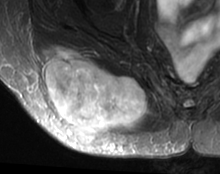
MRI of an extremity soft-tissue mass, one axial slice. Position 22 of 63 along the scan axis. T2-weighted fat-saturated. MR volume resampled by the dataset authors to the PET/CT grid (not the native acquisition matrix). 220 × 174 image matrix, field of view 215 × 170 mm. Female patient. From the clinical record (not read from this slice): histological type: spindle cell suggestive of myxofibrosarcoma; grade: intermediate; site of the primary tumour: right buttock.
Annotated regions visible in this slice (expert contour drawn on MRI and transferred to this co-registered scan by the dataset authors):
- gross tumour volume (mass): box from (x=42, y=45) to (x=149, y=144) px